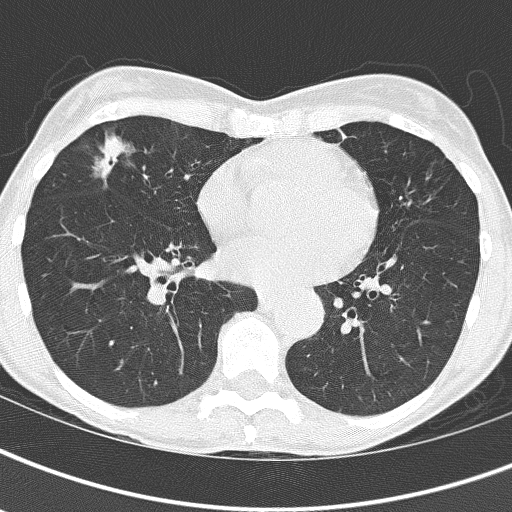
Low-dose screening chest CT, axial slice; first (baseline) screen; lung window (W 1500 / L -600 HU); 2 mm slice thickness; lung (sharp) reconstruction kernel (B60f); slice 96 of 161 in the series. Female participant, aged 67 years at enrolment.
• Lesion marked by an expert reader, bounding box (x1, y1, x2, y2) in pixels: (86, 128, 177, 209).
• Screening reader's record for this exam: no non-calcified nodule ≥4 mm recorded.
• Official screen result: negative screen, significant abnormalities not suspicious for lung cancer.